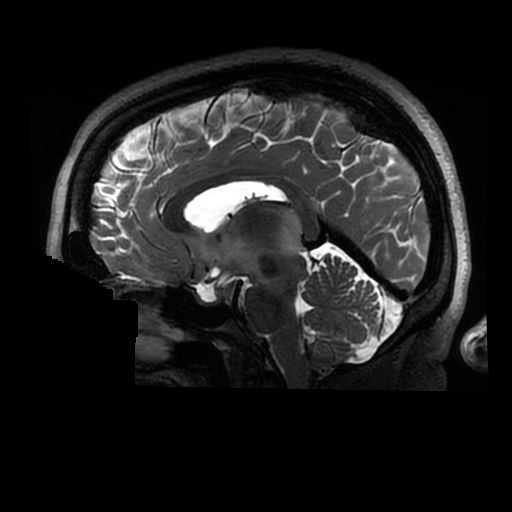
Brain MRI from a brain-tumour surgery series, one sagittal slice; position 156 of 320 along the scan axis; 0.6 mm slice thickness; 512 × 512 image matrix, field of view 240 × 240 mm. From the clinical record (not read from this slice): histopathology: Astrocytoma; WHO grade: 2; IDH mutation: yes.
Annotated regions visible in this slice (manually delineated by an expert):
- tumour: box from (x=277, y=208) to (x=302, y=257) px